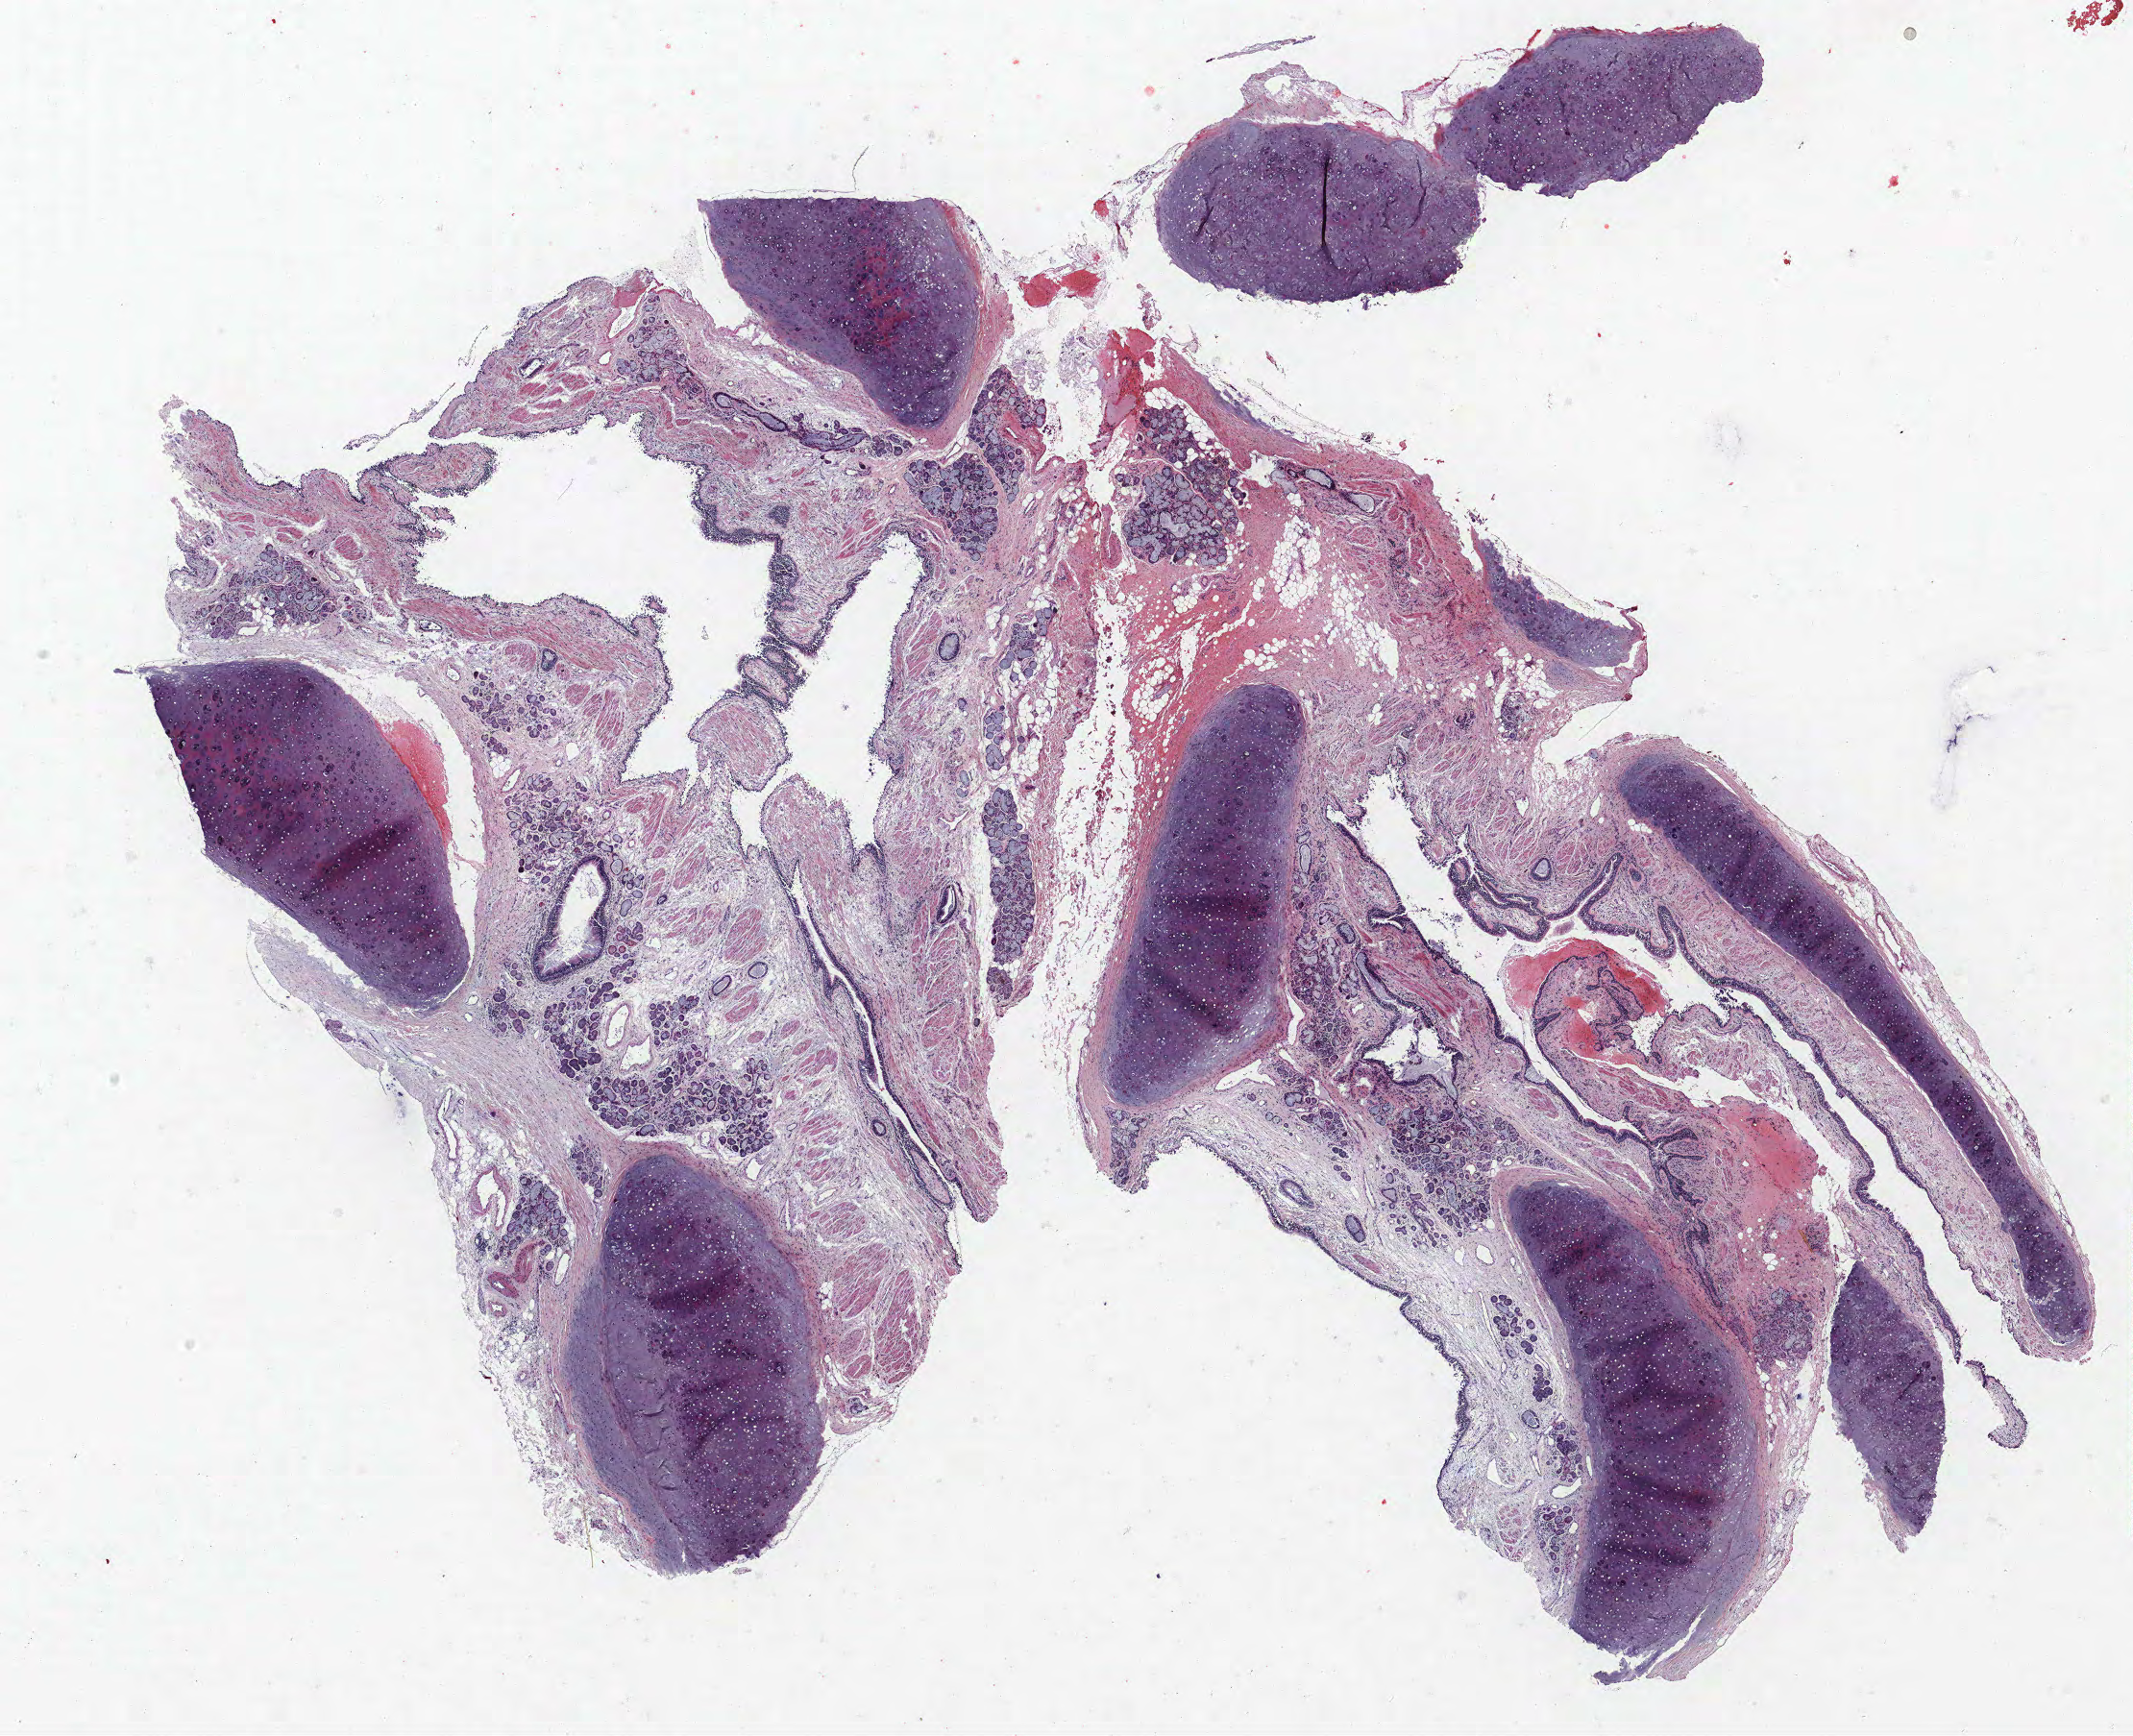
H&E-stained whole-slide image, low-resolution overview of the scanned area, about 17.8 x 14.5 mm, FFPE section, lung. Female patient, aged 63 at enrolment. Grade: moderately differentiated (G2).
Tumour size (pathology): 28 mm. Primary tumour location (clinical record): right lower lobe. ICD-O-3 topography: lower lobe of lung (C34.3). Participant's lung-cancer diagnosis: Mucinous adenocarcinoma. Stage (AJCC 6th edition): IIA.